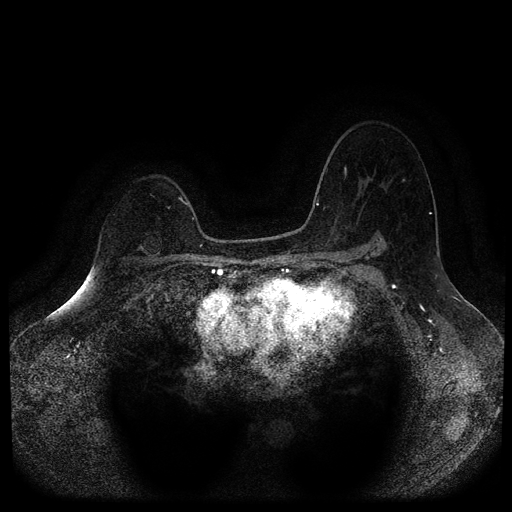
Breast MRI (dynamic contrast-enhanced, multi-phase), one axial slice; position 74 of 116 along the scan axis; dynamic contrast-enhanced series, time point 2 of 5 at this slice position (early post-contrast); 1.5 T; TE 2.6 ms, TR 5.4 ms; 2 mm slice thickness; 512 × 512 image matrix. Female patient, age 64 years.
Outlined on this slice (semi-automatic segmentation, software-assisted and operator-edited):
- breast lesion (labelled benign in the annotation): bounding box (x1, y1, x2, y2) in pixels: (137, 232, 162, 259)